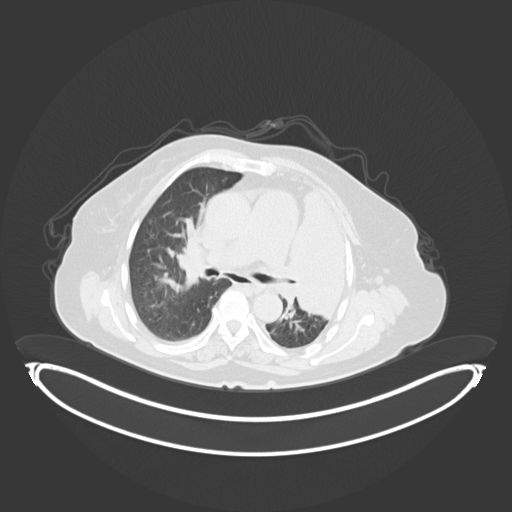
Chest CT, one axial slice. Slice 205 of 284 in the series (ordered by position). Reconstruction kernel B30f. 120 kVp. Lung window (W 1500 / L -600 HU). 3 mm slice thickness. 512 × 512 image matrix. Patient: female, 75 years. Case-level facts recorded for this patient, not image findings: clinical TNM (as recorded): T3 N3 M1.
Outlined on this slice (bounding box drawn by a radiologist):
- lung tumour (recorded histology: adenocarcinoma): bounding box (x1, y1, x2, y2) in pixels: (287, 190, 353, 325)